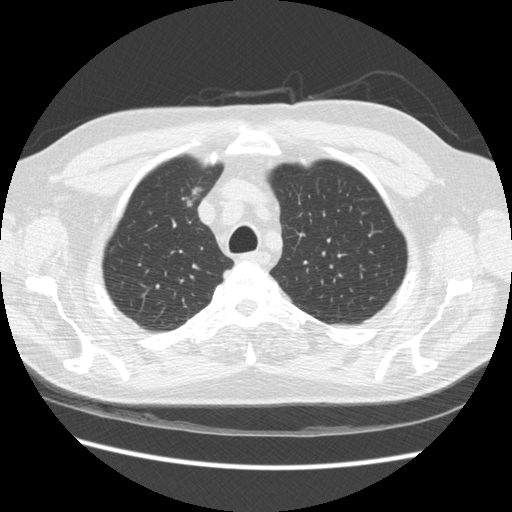
Low-dose screening chest CT, one axial slice; reconstruction kernel STANDARD; 120 kVp; lung window (W 1500 / L -600 HU); 2.5 mm slice thickness; 512 × 512 image matrix, field of view 360 × 360 mm.
Annotated regions visible in this slice (expert manual segmentation):
- lesion 1 (tumor, upper lobe of right lung): box from (x=182, y=186) to (x=202, y=206) px